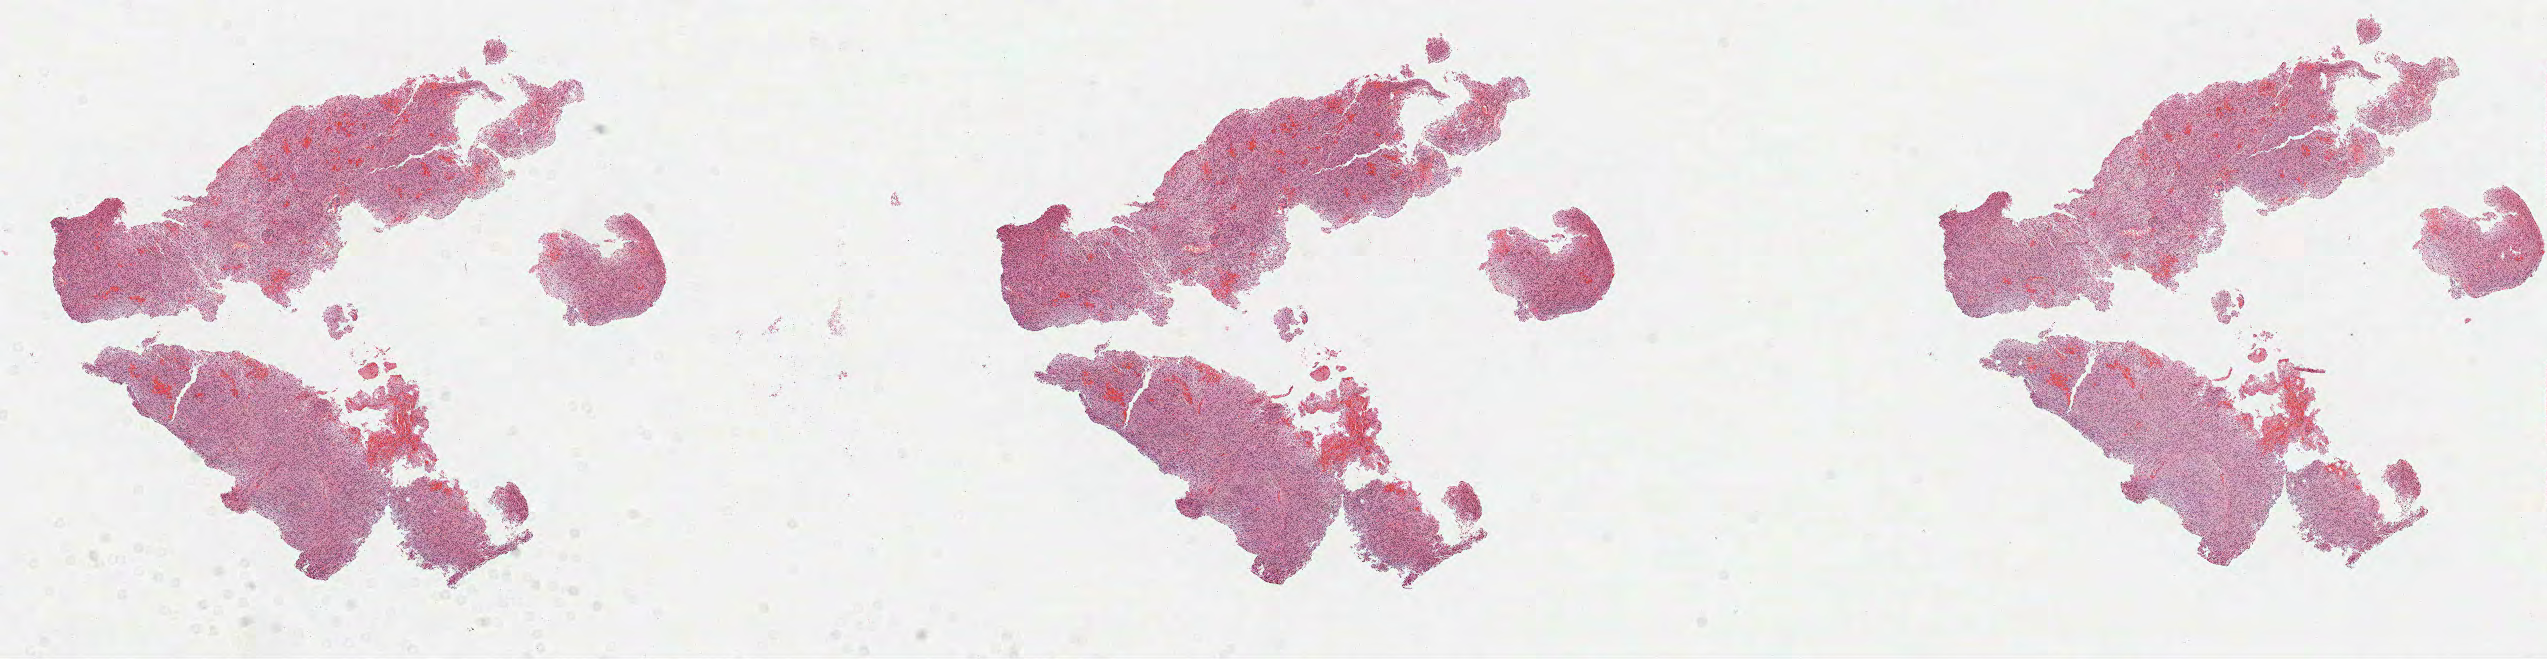
H&E whole-slide image, shown as a low-resolution overview of the whole scanned area (about 20.5 x 5.3 mm, acquisition: 40x scan). Formalin-fixed paraffin-embedded (FFPE) diagnostic section. Primary tumour sample from the brain. Female patient; age at initial diagnosis 34 years. Histologic grade: G3 (poorly differentiated).
Histologic diagnosis: Astrocytoma, anaplastic.